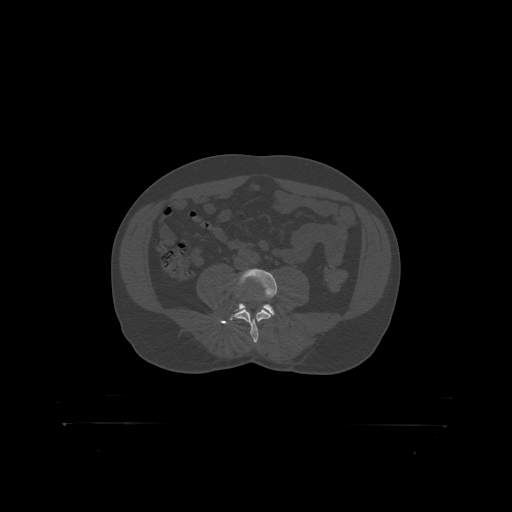
CT including the spine, one axial slice. Slice 224 of 399 in the series (ordered by position). 120 kVp. Bone window (W 1800 / L 400 HU). 1.25 mm slice thickness. 512 × 512 image matrix, field of view 650 × 650 mm. Male patient, age 46 years. From the clinical record (not read from this slice): primary cancer: skin.
Annotated regions visible in this slice (semi-automatically segmented with operator editing):
- L4 vertebra: bounding box [x1, y1, x2, y2] px = [236, 269, 277, 319]
- L5 vertebra: [237, 304, 275, 316]